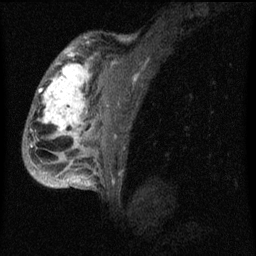
Breast MRI (dynamic contrast-enhanced), one sagittal slice; slice 44 of 60 in the series (ordered by position); dynamic contrast-enhanced series, image 2 of 4 at this slice position (ordered by acquisition); 1.5 T; TE 4.2 ms, TR 8 ms; 256 × 256 image matrix. Patient: female, 50 years.
Structures marked on this image (semi-automatic segmentation, software-assisted and operator-edited):
- analysis volume of interest (the breast-tissue region the enhancement analysis was run in; not a lesion): bounding box <26,44,124,177> (left, top, right, bottom; pixels)
- tumour enhancement mask (voxels above the 70 % enhancement threshold inside the analysis volume of interest): <32,46,109,177>